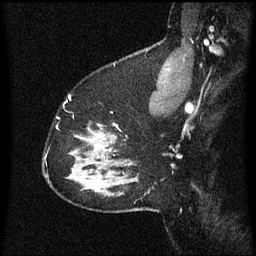
Breast MRI (dynamic contrast-enhanced), one sagittal slice; slice 48 of 60 in the series (ordered by position); dynamic contrast-enhanced series, image 2 of 3 at this slice position (ordered by acquisition); 1.5 T; TE 4.2 ms, TR 8.4 ms; 2 mm slice thickness; 256 × 256 image matrix, field of view 200 × 200 mm. Patient: female, 37 years. Case-level facts recorded for this patient, not image findings: setting: breast cancer imaged before/during neoadjuvant chemotherapy; receptor status: HR-positive, HER2-negative.
Structures marked on this image (semi-automatically segmented with operator editing):
- analysis volume of interest (the breast-tissue region the enhancement analysis was run in; not a lesion): bounding box [x1, y1, x2, y2] px = [94, 124, 118, 157]
- tumour enhancement mask (voxels above the 70 % enhancement threshold inside the analysis volume of interest): [103, 136, 116, 139]